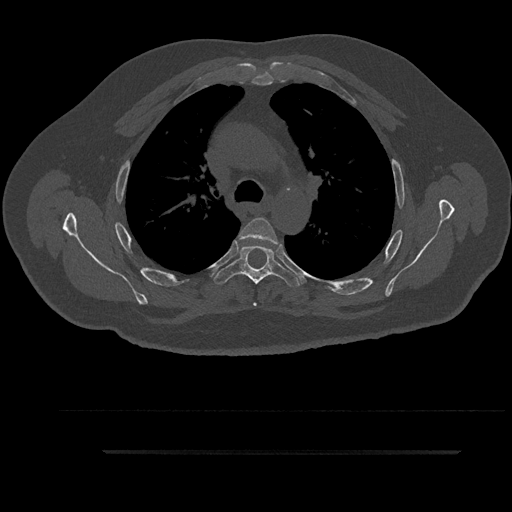
CT including the spine, one axial slice. Position 643 of 797 along the scan axis. 120 kVp. Bone window (W 1800 / L 400 HU). 0.5 mm slice thickness. 512 × 512 image matrix, field of view 432 × 432 mm. Patient: male, 63 years. From the clinical record (not read from this slice): primary cancer: renal.
Outlined on this slice (semi-automatically segmented with operator editing):
- T4 vertebra: bounding box [x1, y1, x2, y2] px = [238, 217, 280, 306]
- T5 vertebra: [215, 245, 299, 289]